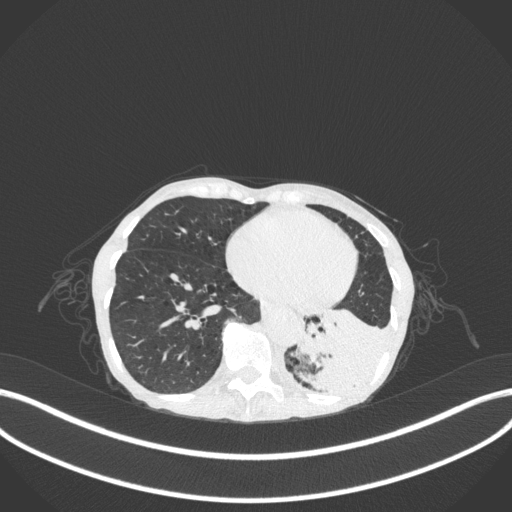
Chest CT, one axial slice. Position 77 of 347 along the scan axis. 120 kVp. Lung window (W 1500 / L -600 HU). 1 mm slice thickness. 512 × 512 image matrix, field of view 400 × 400 mm. Female patient, age 70 years. Case-level facts recorded for this patient, not image findings: clinical TNM (as recorded): T3 N0 M0.
Annotated regions visible in this slice (bounding box drawn by a radiologist):
- lung tumour (recorded histology: small cell carcinoma): bounding box (x1, y1, x2, y2) in pixels: (291, 303, 392, 406)